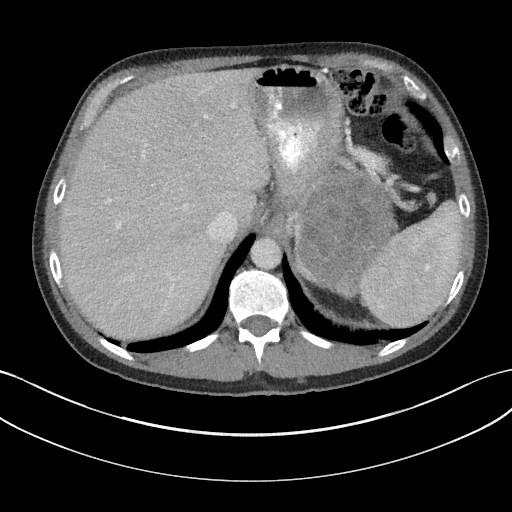
Contrast-enhanced abdominal CT, one axial slice; position 127 of 147 along the scan axis; reconstruction kernel I31f/3; intravenous contrast given; soft-tissue window (W 400 / L 40 HU); 3 mm slice thickness; 512 × 512 image matrix, field of view 384 × 384 mm. Patient: male, 58 years. Case-level facts recorded for this patient, not image findings: diagnosis: adrenocortical carcinoma; tumour side: left adrenal; tumour size at pathology: 22 cm; Ki-67 index: 26 %; stage (as recorded): 2.
Annotated regions visible in this slice (semi-automatic segmentation, software-assisted and operator-edited):
- mass: bounding box [x1, y1, x2, y2] px = [296, 173, 389, 295]